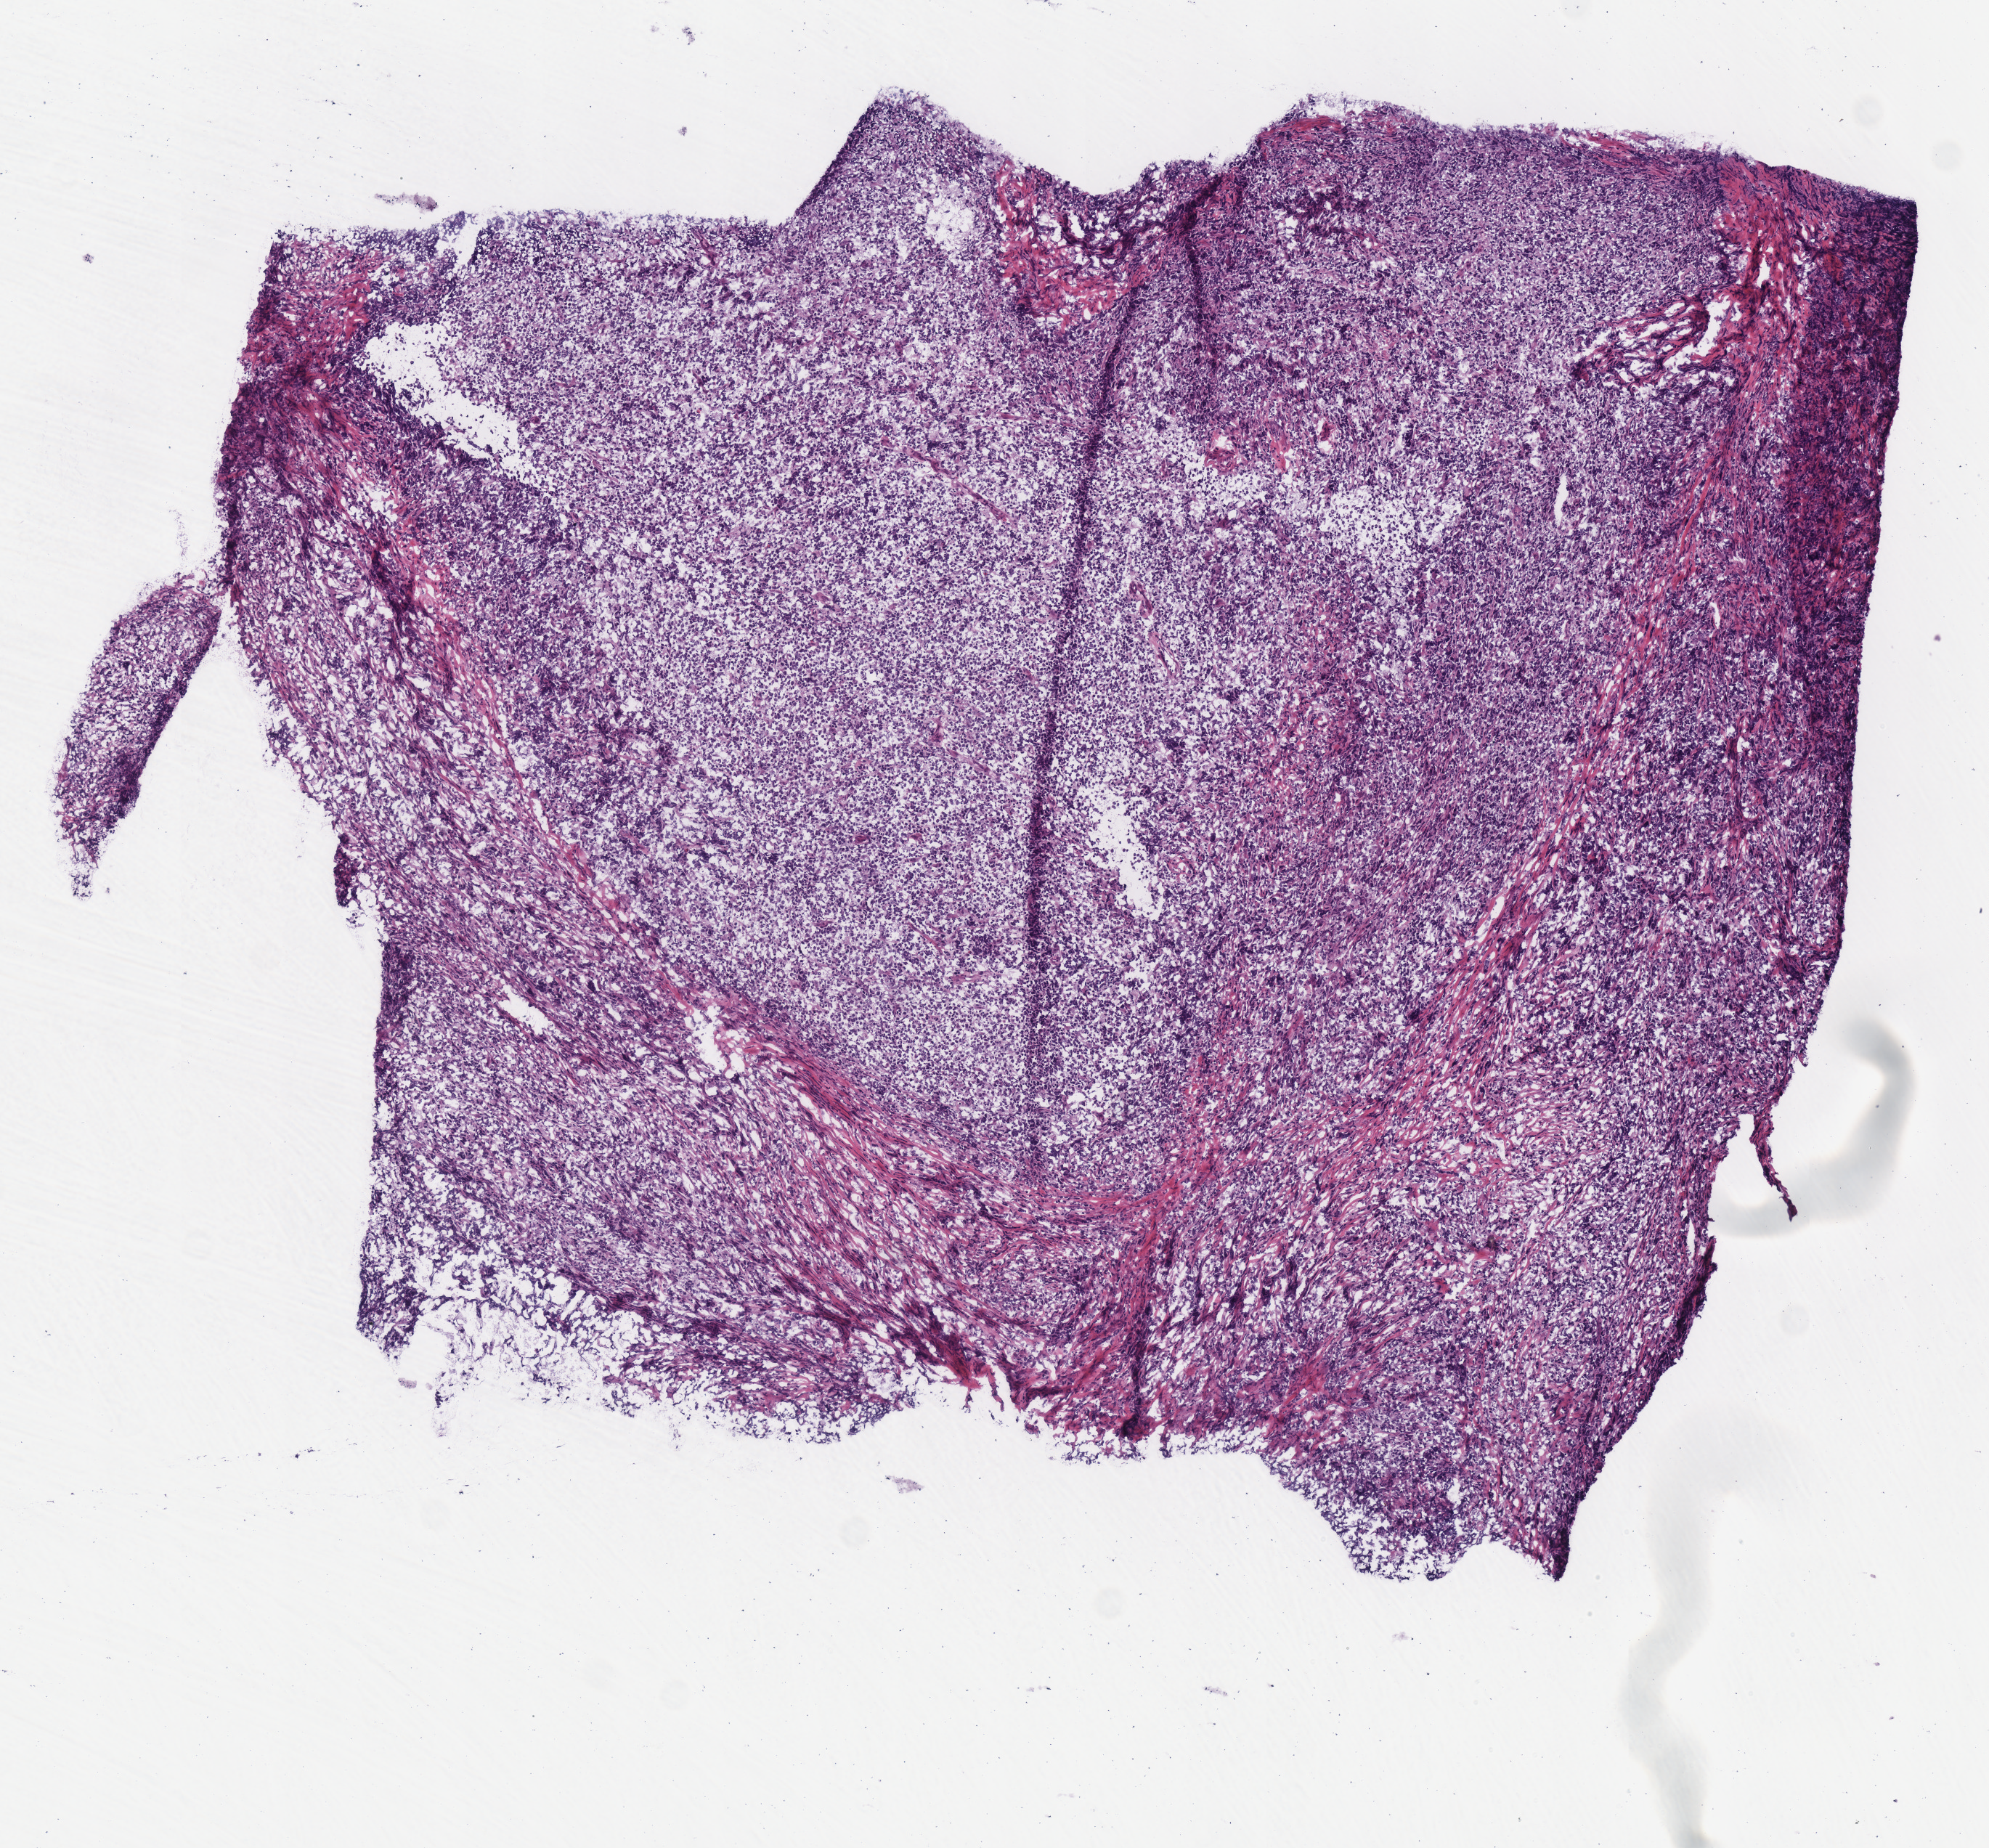
Digitized H&E tissue section (whole slide), low-resolution overview of the scanned area, about 5.4 x 5.0 mm (acquisition: 40x scan); frozen section; primary tumour sample from the lymphoid tissue. Patient: male, age at initial diagnosis 42 years. Slide review estimates, as recorded: tumour cells 85%, tumour nuclei 90%, normal cells 0%, stromal cells 15%, necrosis 0%.
Diagnosis: Diffuse large B-cell lymphoma, NOS (small intestine, NOS).